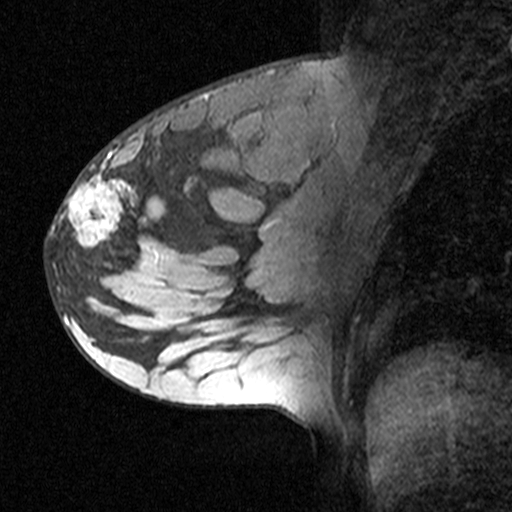
Breast MRI (dynamic contrast-enhanced), one sagittal slice; slice 21 of 44 in the series (ordered by position); dynamic contrast-enhanced study with each time point stored as its own series, time point 2 of 3 at this slice position (early post-contrast, ordered by acquisition time); 1.5 T; TE 4.5 ms, TR 11 ms; 512 × 512 image matrix, field of view 200 × 200 mm. Patient: female, 27 years. From the clinical record (not read from this slice): setting: breast cancer imaged before/during neoadjuvant chemotherapy; receptor status: HR-positive, HER2-negative.
Outlined on this slice (semi-automatic segmentation, software-assisted and operator-edited):
- analysis volume of interest (the breast-tissue region the enhancement analysis was run in; not a lesion): box from (x=46, y=162) to (x=163, y=271) px
- tumour enhancement mask (voxels above the 90 % enhancement threshold inside the analysis volume of interest): (x=53, y=162)–(x=142, y=254)